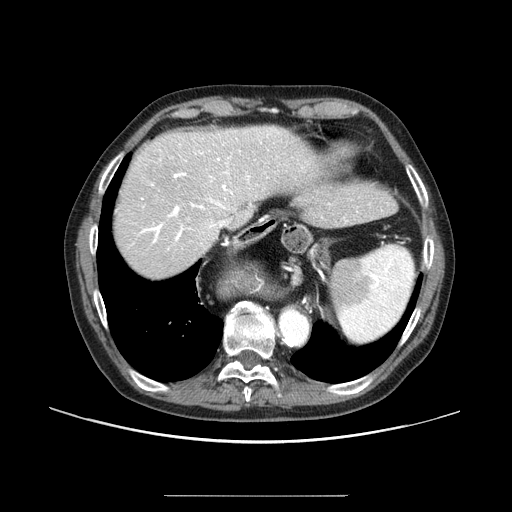
Contrast-enhanced abdominal CT (liver protocol), one axial slice. Slice 72 of 91 in the series (ordered by position). 100 kVp. One of 2 acquisitions stored at this slice position. Soft-tissue window (W 400 / L 40 HU). 2.5 mm slice thickness. 512 × 512 image matrix. Case-level facts recorded for this patient, not image findings: diagnosis: hepatocellular carcinoma (patient treated with transarterial chemoembolisation; whether this scan precedes or follows treatment is not stated here); TNM stage (as recorded): Stage-I; Child-Pugh class: A.
Structures marked on this image (semi-automatically segmented with operator editing):
- abdominal aorta: bounding box [x1, y1, x2, y2] px = [280, 309, 307, 343]
- liver parenchyma outside the tumour (the mass and vessels are separate outlines, so this box may not span the whole liver): [114, 126, 320, 278]
- liver vessels: [138, 129, 279, 250]